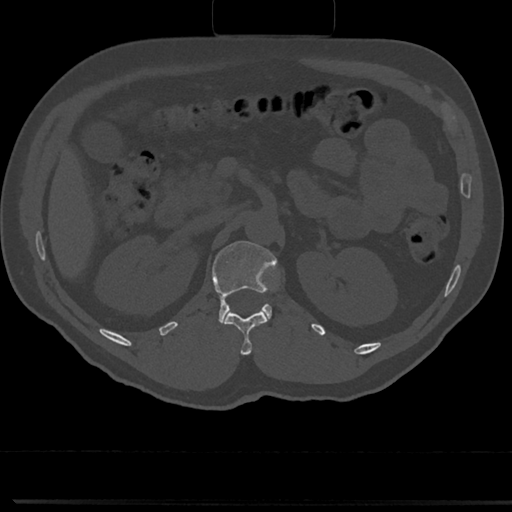
CT including the spine, one axial slice. Position 110 of 817 along the scan axis. Reconstruction kernel Br40s/3. 120 kVp. Bone window (W 1800 / L 400 HU). 0.5 mm slice thickness. 512 × 512 image matrix, field of view 355 × 355 mm. Patient: male, 61 years. From the clinical record (not read from this slice): primary cancer: prostate.
Structures marked on this image (semi-automatic segmentation, software-assisted and operator-edited):
- L1 vertebra: bounding box [x1, y1, x2, y2] px = [213, 240, 278, 326]
- T12 vertebra: [224, 311, 268, 354]